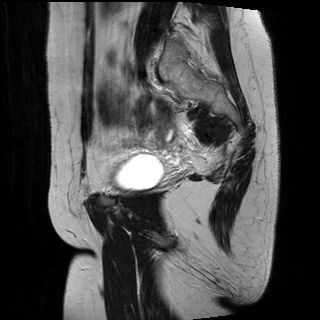
Pelvic MRI for cervical cancer, one sagittal slice; slice 24 of 34 in the series (ordered by position); T2-weighted; 1.5 T; TE 89 ms, TR 3320 ms; 4 mm slice thickness; 320 × 320 image matrix, field of view 260 × 260 mm. Female patient, age 49 years.
Outlined on this slice (manually delineated by an expert):
- uterus and cervix: bounding box (x1, y1, x2, y2) in pixels: (136, 94, 172, 137)